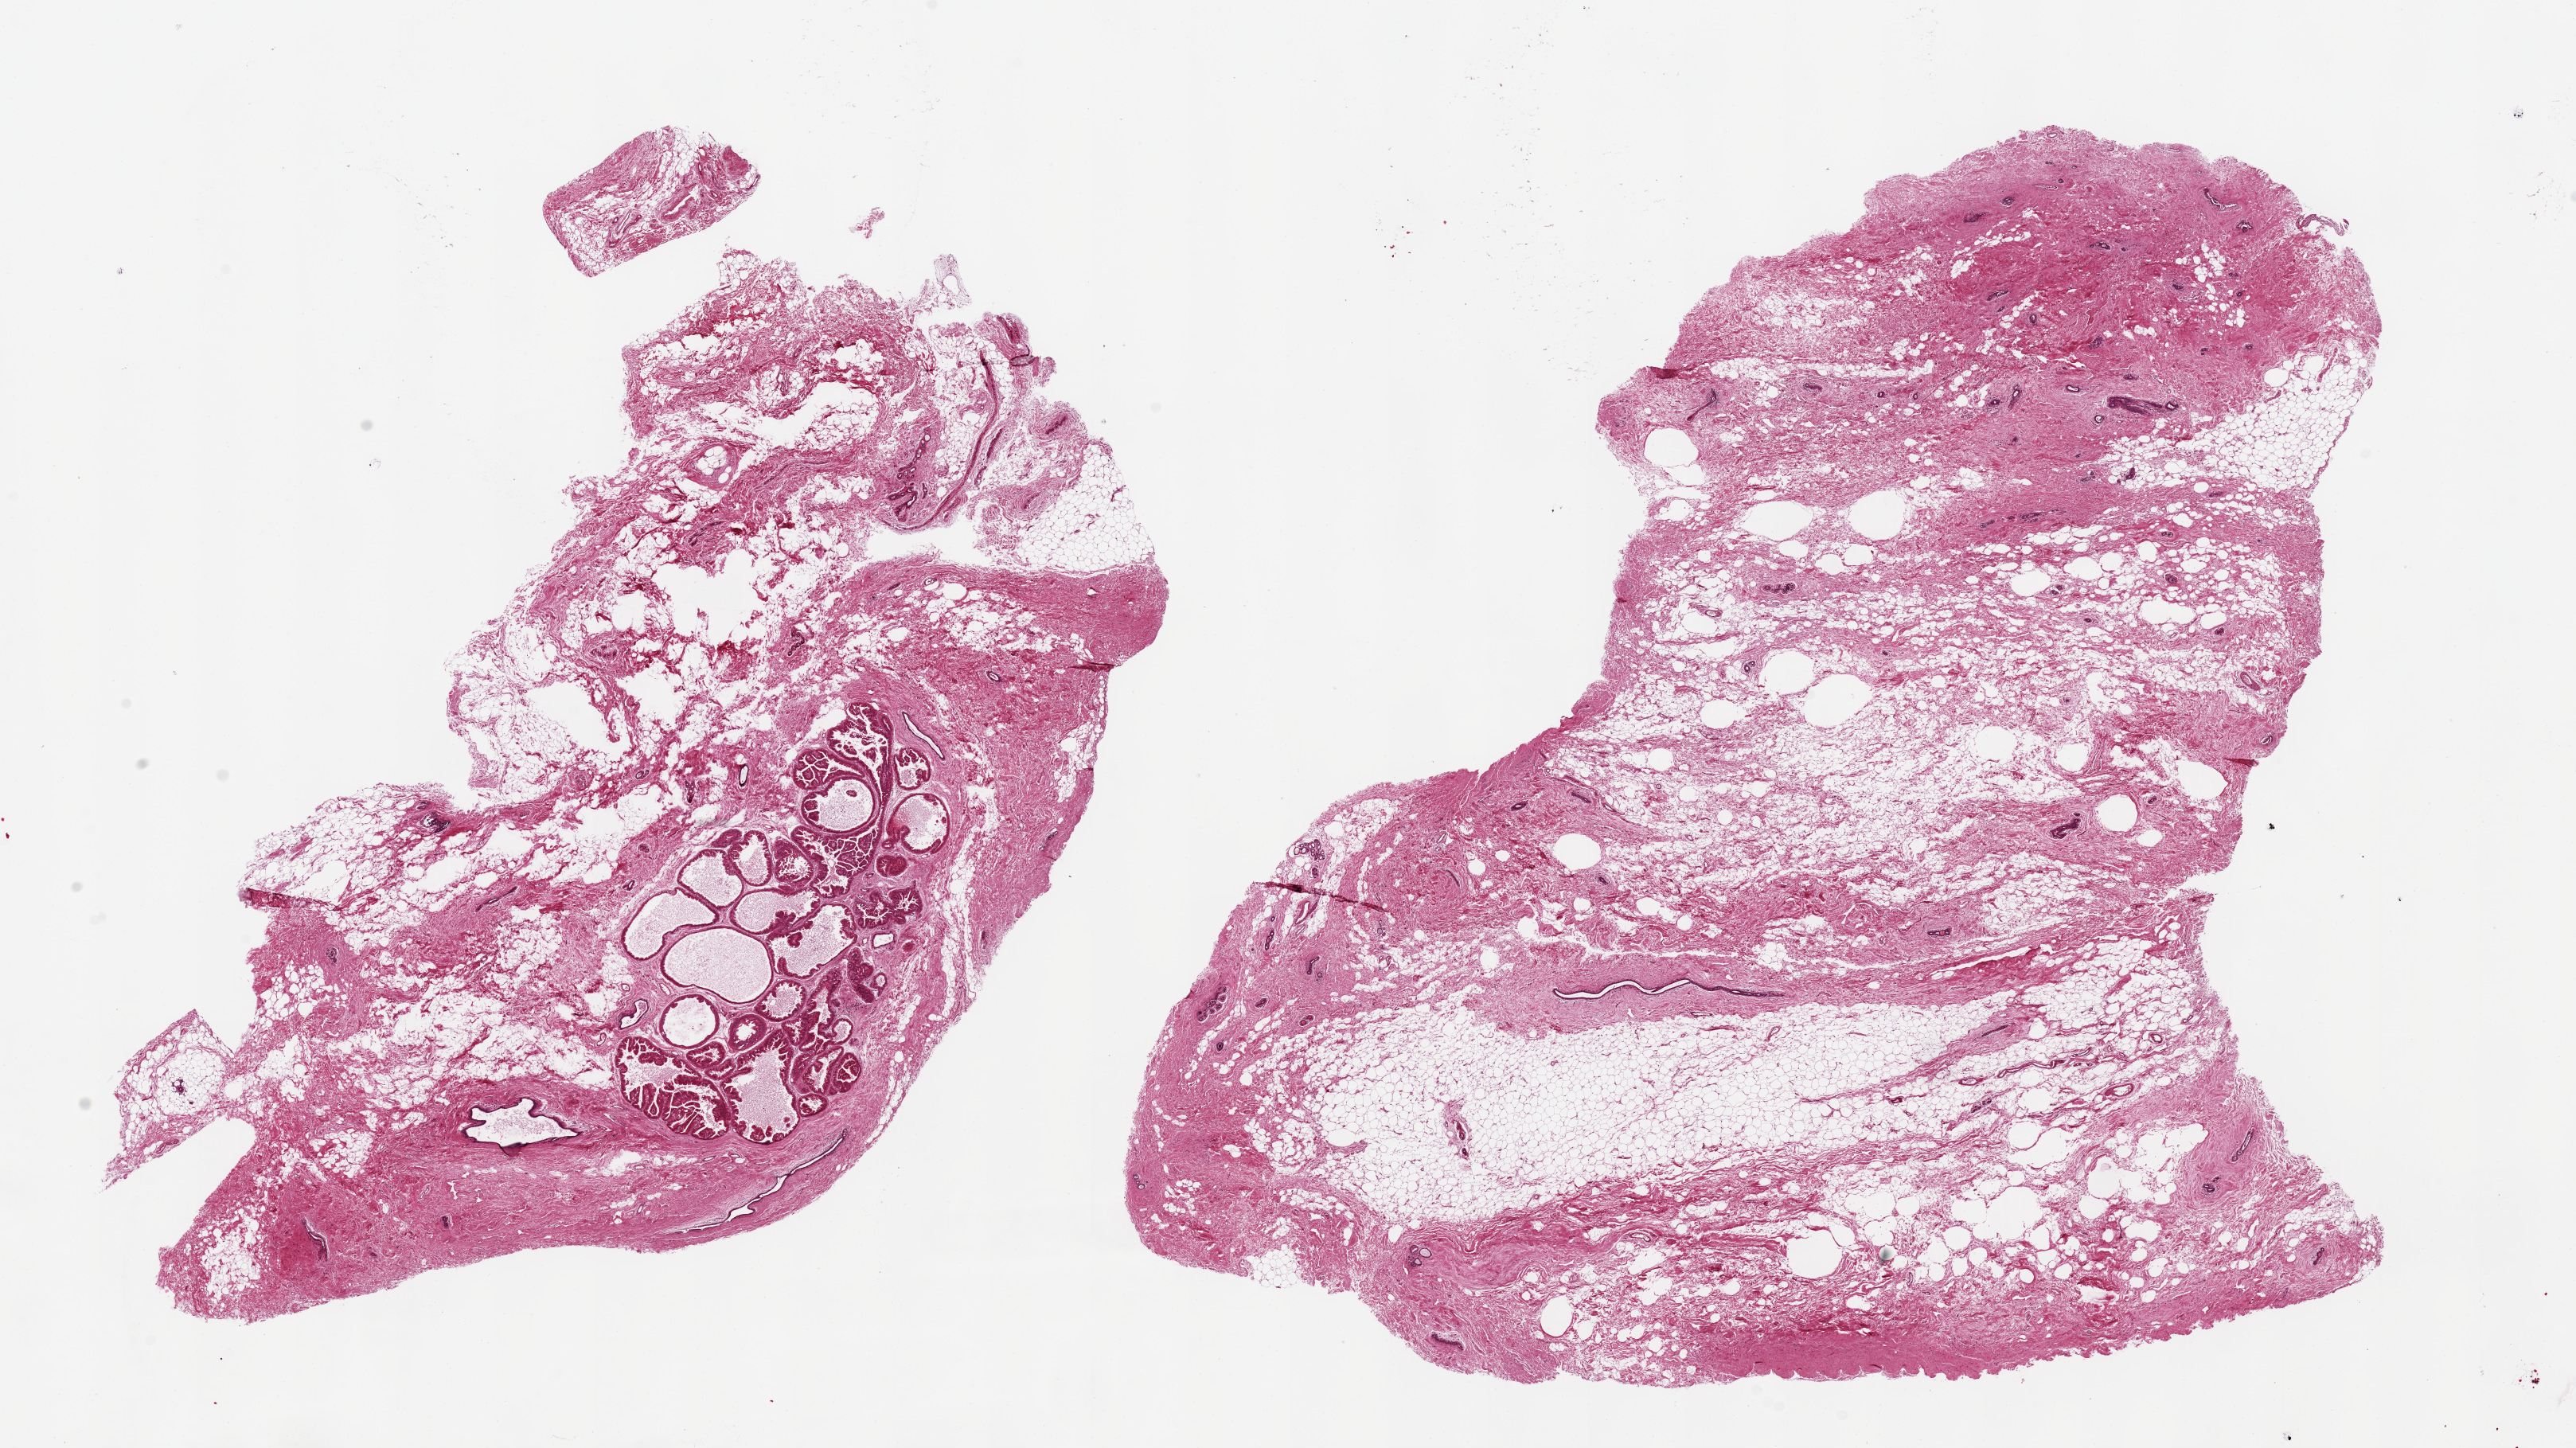
Digitized hematoxylin and eosin (H&E)-stained section, brightfield, low-resolution overview of the scanned area, about 25.6 x 14.4 mm (acquisition: 20x scan); PAXgene-fixed paraffin-embedded (PFPE) section; section of breast (target tissue); tissue donor sample. Donor: female.
Reviewer comment on this tissue sample: 2 pieces, 13x8 & 13x12.5mm; 5mm focus apocrine metaplasia in one section, fibrosystic change.